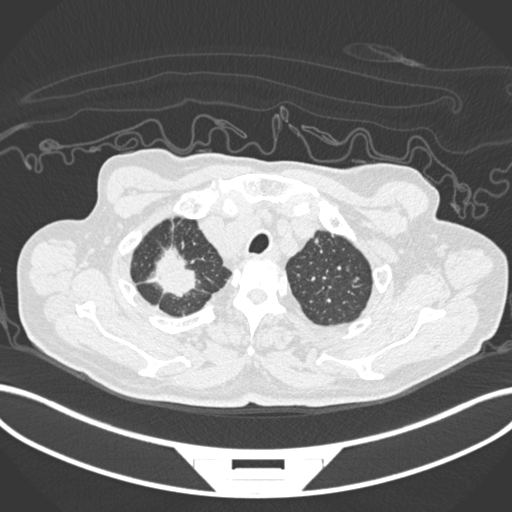
Chest CT, one axial slice. Position 192 of 207 along the scan axis. Reconstruction kernel B30f. Lung window (W 1500 / L -600 HU). 1 mm slice thickness. 512 × 512 image matrix, field of view 400 × 400 mm. Male patient, age 69 years. Case-level facts recorded for this patient, not image findings: clinical TNM (as recorded): T1c N1 M1.
Annotated regions visible in this slice (rectangle marked by the reading radiologist):
- lung tumour (recorded histology: adenocarcinoma): bounding box [x1, y1, x2, y2] px = [148, 243, 202, 300]